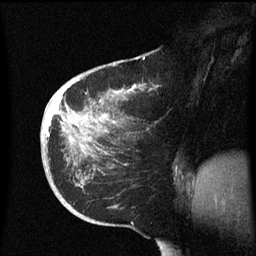
Breast MRI (dynamic contrast-enhanced), one sagittal slice; slice 26 of 60 in the series (ordered by position); dynamic contrast-enhanced series, image 2 of 3 at this slice position (ordered by acquisition); 1.5 T; TE 4.2 ms, TR 8.4 ms; 2.3 mm slice thickness; 256 × 256 image matrix, field of view 200 × 200 mm. Patient: female, 38 years. Case-level facts recorded for this patient, not image findings: setting: breast cancer imaged before/during neoadjuvant chemotherapy; receptor status: HER2-positive.
Annotated regions visible in this slice (semi-automatic segmentation, software-assisted and operator-edited):
- analysis volume of interest (the breast-tissue region the enhancement analysis was run in; not a lesion): bounding box (x1, y1, x2, y2) in pixels: (41, 78, 158, 213)
- tumour enhancement mask (voxels above the 70 % enhancement threshold inside the analysis volume of interest): (48, 84, 143, 151)